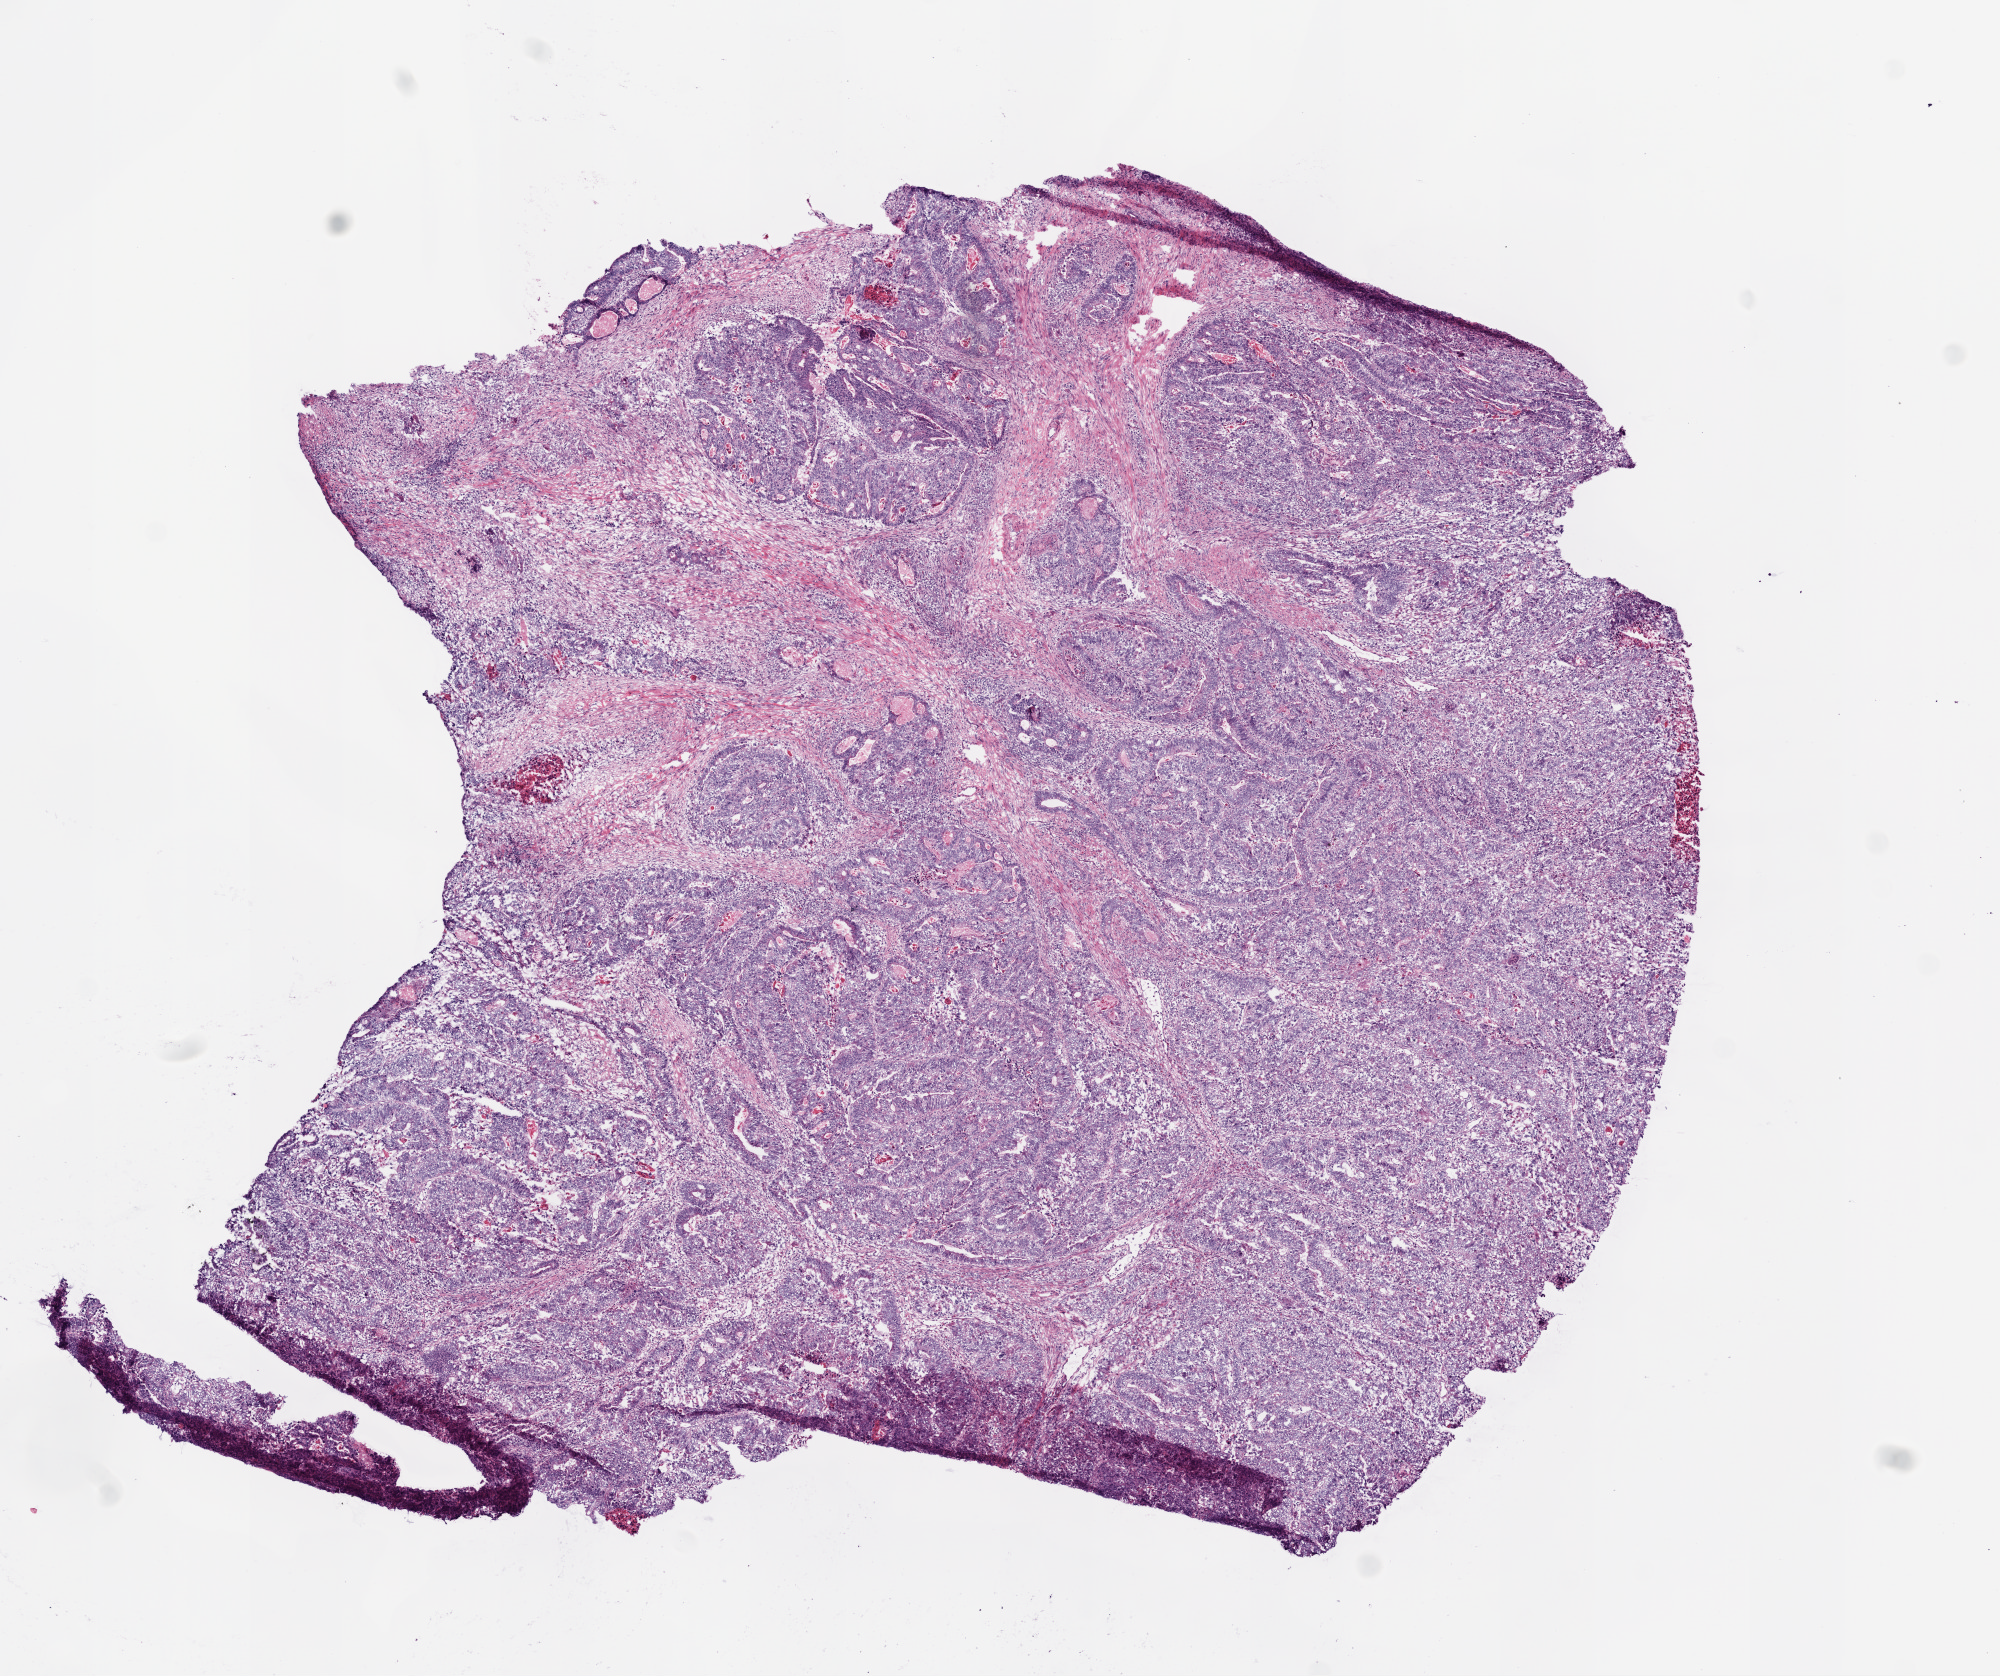
Digitized H&E-stained tissue section (whole slide) — whole scanned area (about 8.0 x 6.7 mm) shown as a low-resolution overview; frozen section from the top of the tissue portion; colon, primary tumour sample. Female, age 61 years at initial diagnosis. Slide review estimates, as recorded: tumour cells 70%, tumour nuclei 80%, normal cells 0%, stromal cells 30%, necrosis 0%.
Lymph nodes positive (case pathology): 0 of 21 examined. AJCC pathologic stage: I (6th edition). Diagnosis: Adenocarcinoma, NOS.